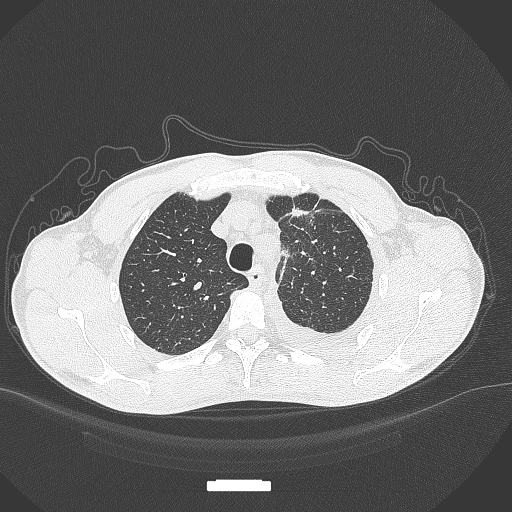
Chest CT, one axial slice. Position 274 of 371 along the scan axis. Reconstruction kernel B70f. 120 kVp. Lung window (W 1500 / L -600 HU). 1 mm slice thickness. 512 × 512 image matrix, field of view 400 × 400 mm. Male patient, age 49 years. From the clinical record (not read from this slice): clinical TNM (as recorded): T1c N1 M1.
Annotated regions visible in this slice (rectangle marked by the reading radiologist):
- lung tumour (recorded histology: adenocarcinoma): box from (x=280, y=207) to (x=322, y=222) px